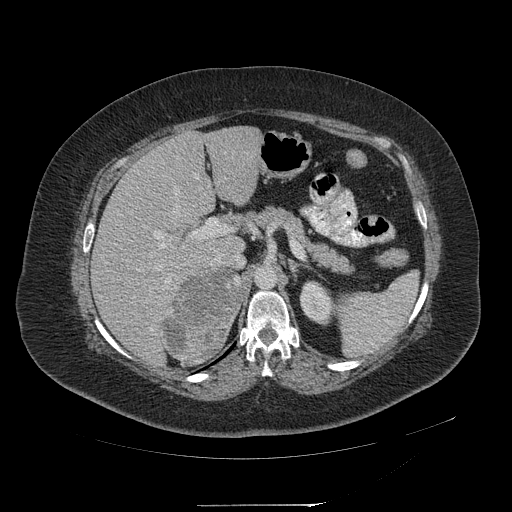
Contrast-enhanced abdominal CT, one axial slice; slice 136 of 217 in the series (ordered by position); reconstruction kernel STANDARD; soft-tissue window (W 400 / L 40 HU); 1.25 mm slice thickness; 512 × 512 image matrix, field of view 453 × 453 mm. Patient: female, 55 years. Case-level facts recorded for this patient, not image findings: diagnosis: adrenocortical carcinoma; tumour side: right adrenal; tumour size at pathology: 11 cm.
Outlined on this slice (semi-automatic segmentation, software-assisted and operator-edited):
- mass: bounding box [x1, y1, x2, y2] px = [163, 270, 239, 365]